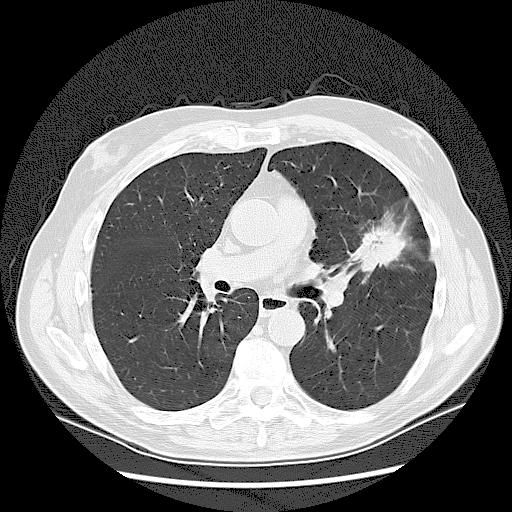
Low-dose screening chest CT, one axial slice; position 73 of 132 along the scan axis; reconstruction kernel LUNG; lung window (W 1500 / L -600 HU); 2.5 mm slice thickness; 512 × 512 image matrix, field of view 380 × 380 mm.
Outlined on this slice (manually delineated by an expert):
- lesion 1 (tumor, upper lobe of left lung): bounding box (x1, y1, x2, y2) in pixels: (359, 224, 407, 270)